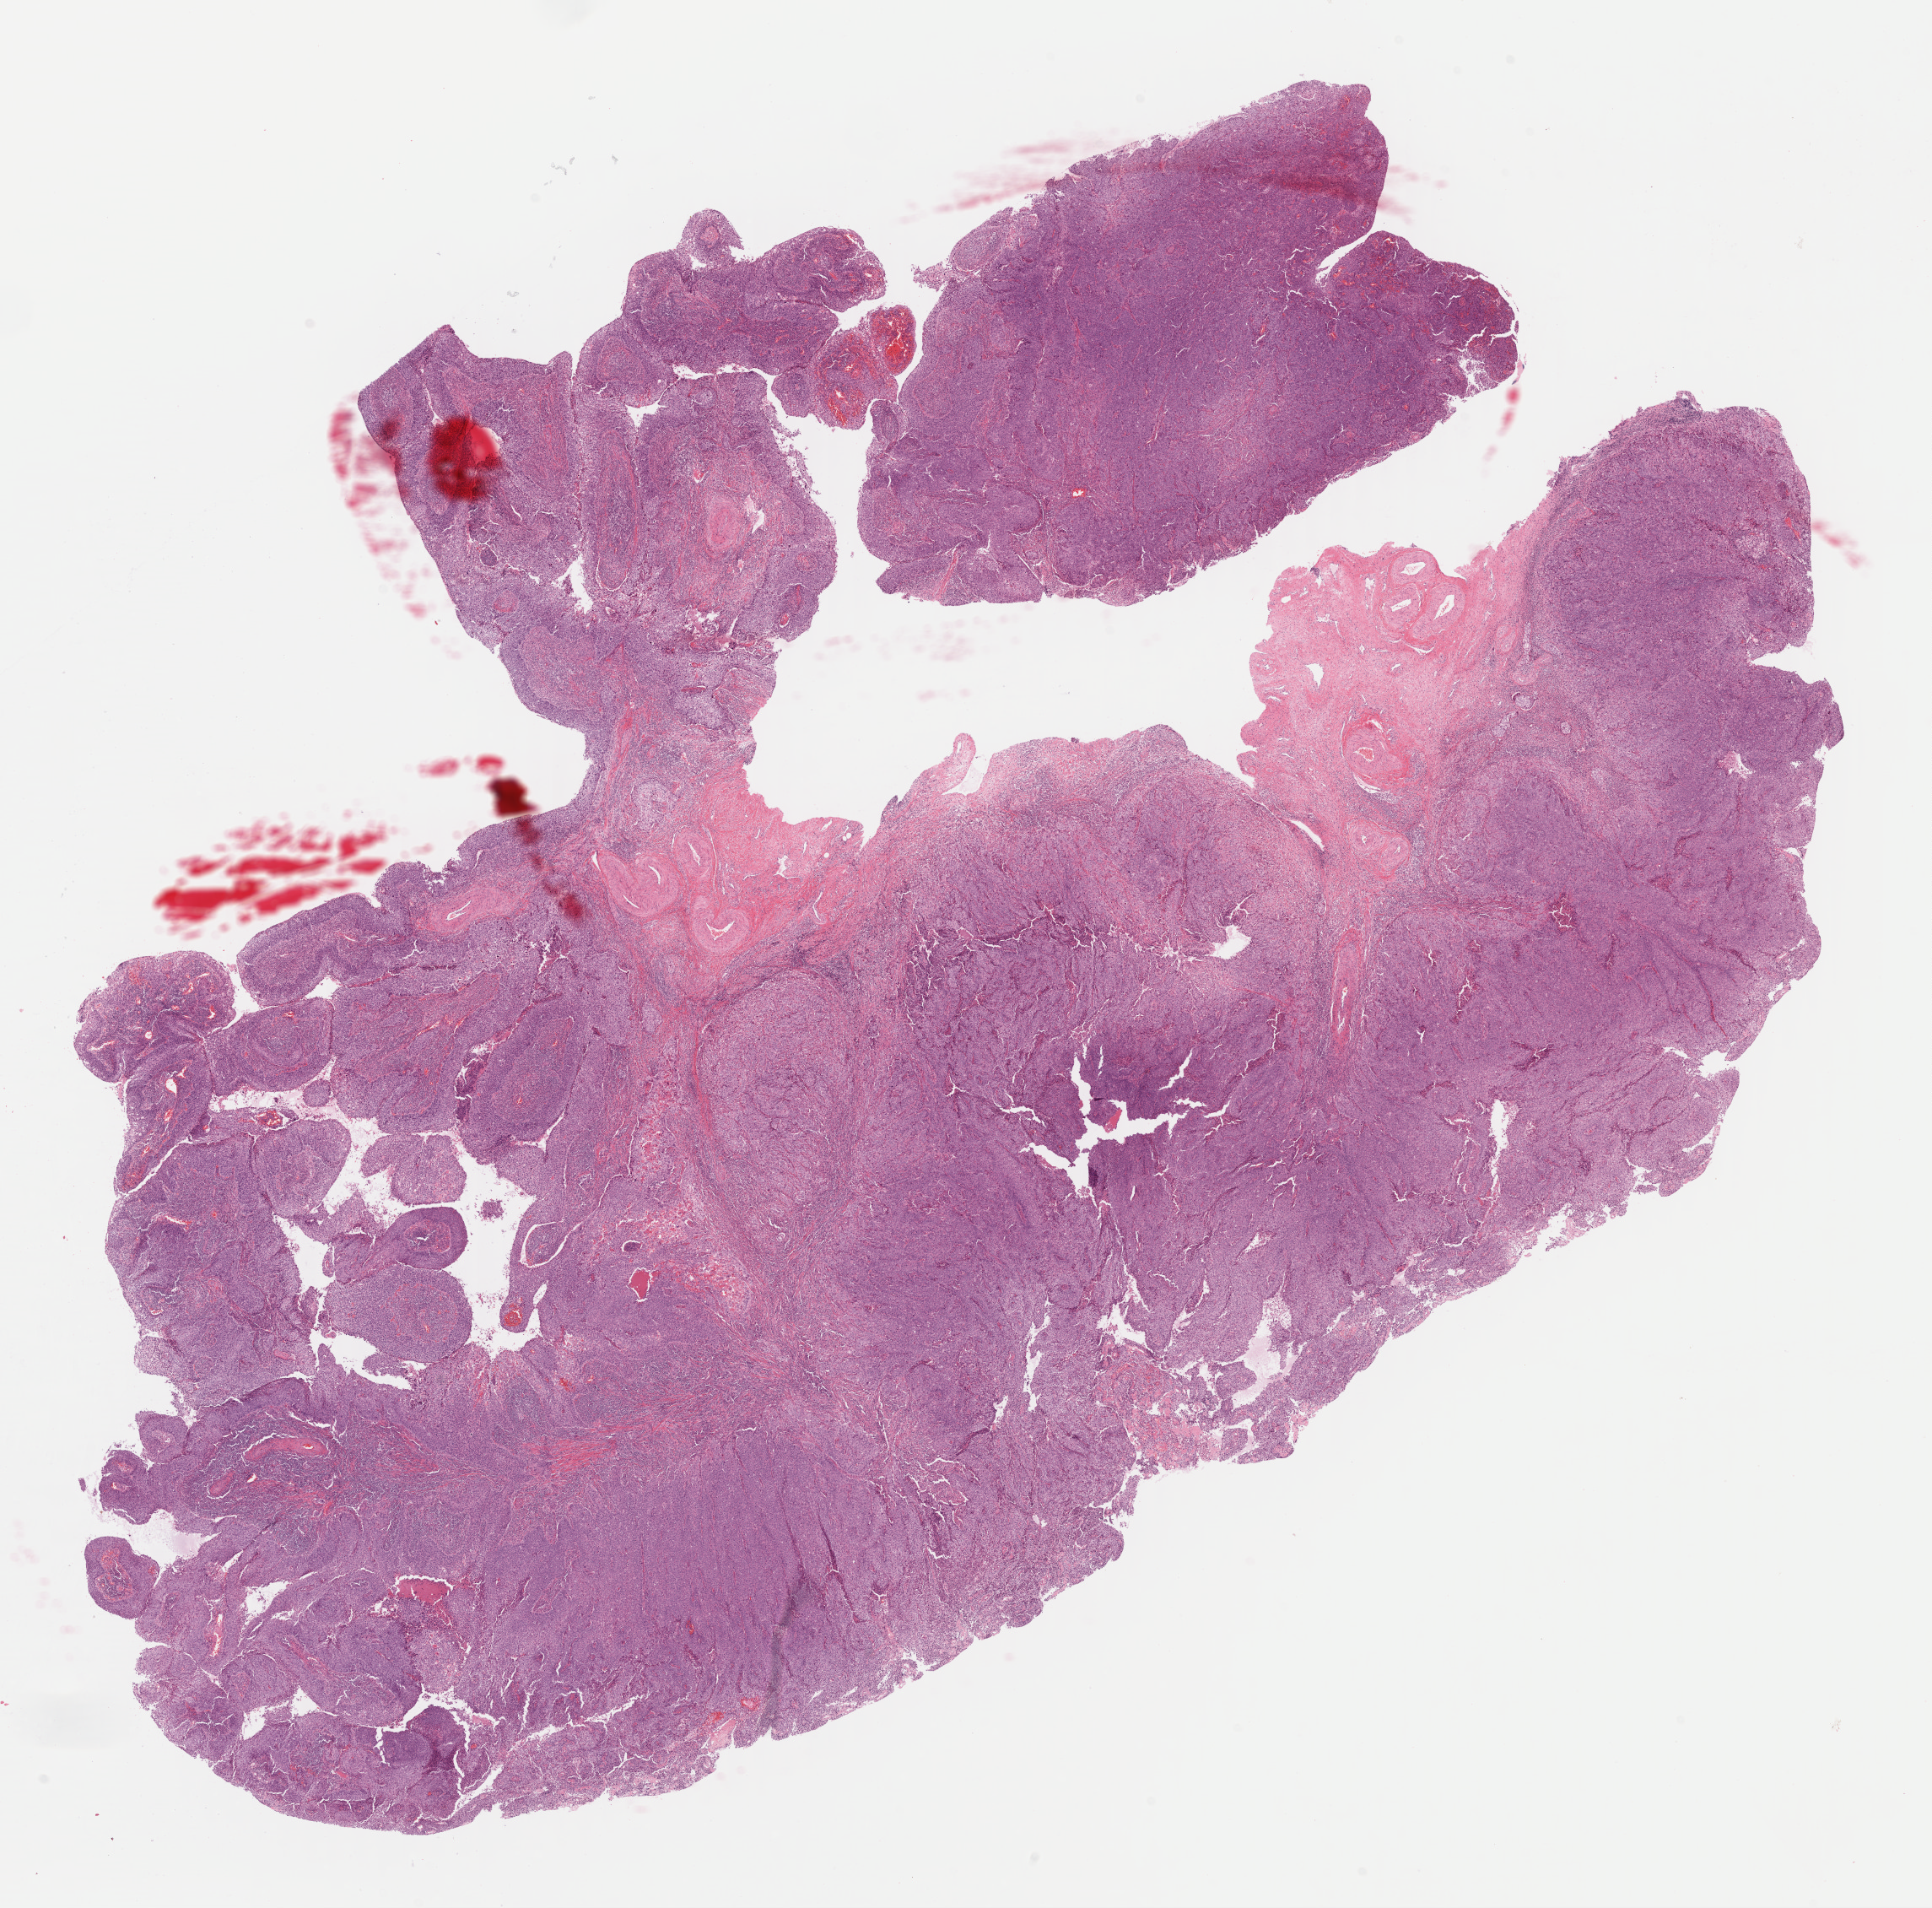
Digitized H&E tissue section (whole slide) — a low-resolution overview of the entire scanned area, about 18.0 x 17.8 mm (acquisition: 40x scan), formalin-fixed paraffin-embedded (FFPE) diagnostic section, primary tumour sample from the cervix. Female patient; age at initial diagnosis 39 years.
Diagnosis: Squamous cell carcinoma, NOS (exocervix).